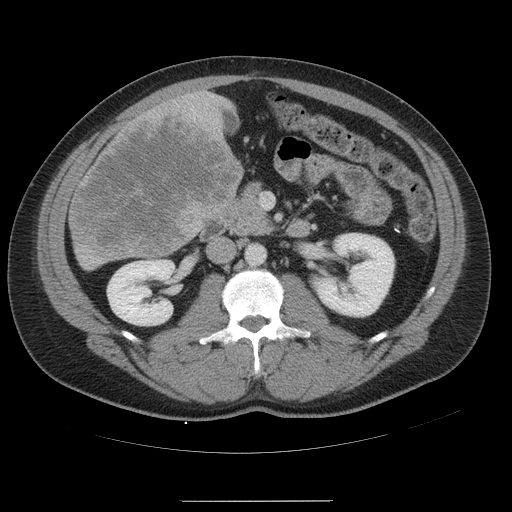
Contrast-enhanced abdominal CT, one axial slice; position 20 of 54 along the scan axis; intravenous contrast given; soft-tissue window (W 400 / L 40 HU); 5 mm slice thickness; 512 × 512 image matrix, field of view 436 × 436 mm. Male patient, age 40 years. From the clinical record (not read from this slice): diagnosis: colorectal cancer liver metastases, imaged before liver resection; multiple liver metastases: no.
Structures marked on this image (outlined manually by an expert reader):
- liver: bounding box [x1, y1, x2, y2] px = [69, 92, 244, 270]
- liver metastasis: [69, 109, 242, 260]